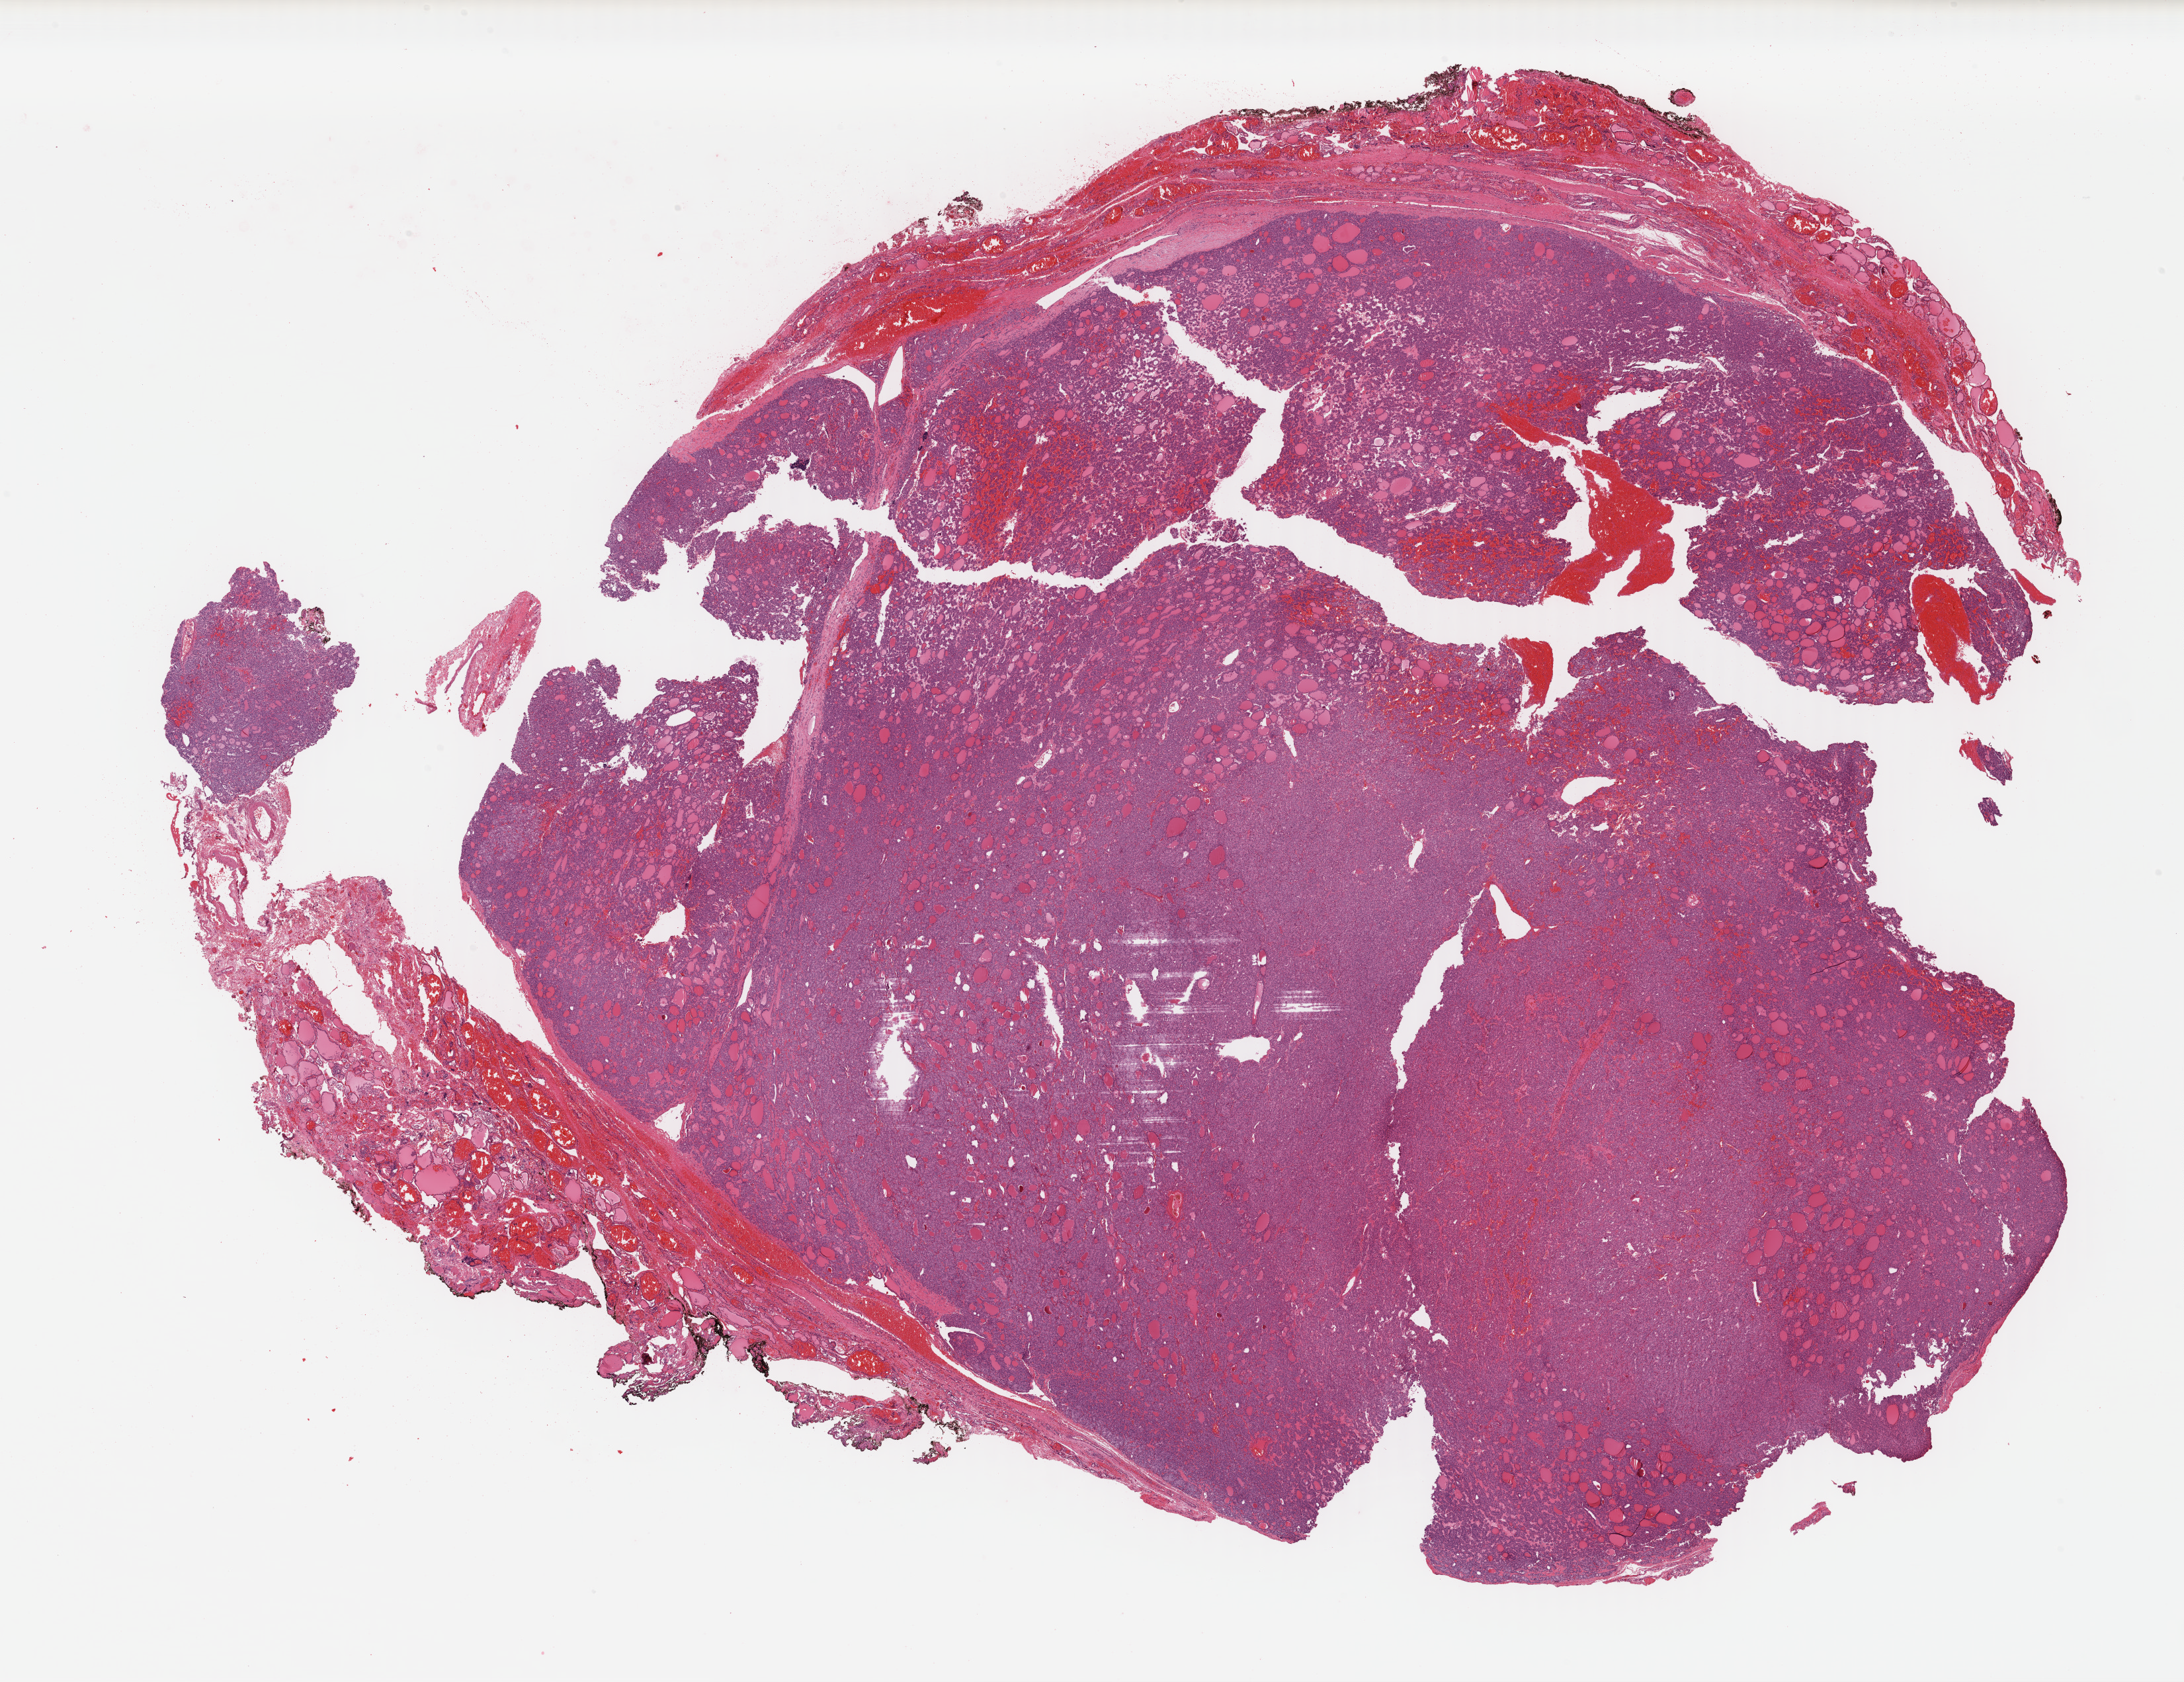
Whole-slide histology image, H&E — whole scanned area (about 26.0 x 20.0 mm, from a 40x scan) shown as a low-resolution overview; FFPE section; primary tumour sample from the thyroid. Female patient; age at initial diagnosis 29 years.
Diagnosis: Papillary adenocarcinoma, NOS (thyroid gland). Laterality: left. AJCC pathologic stage: I.